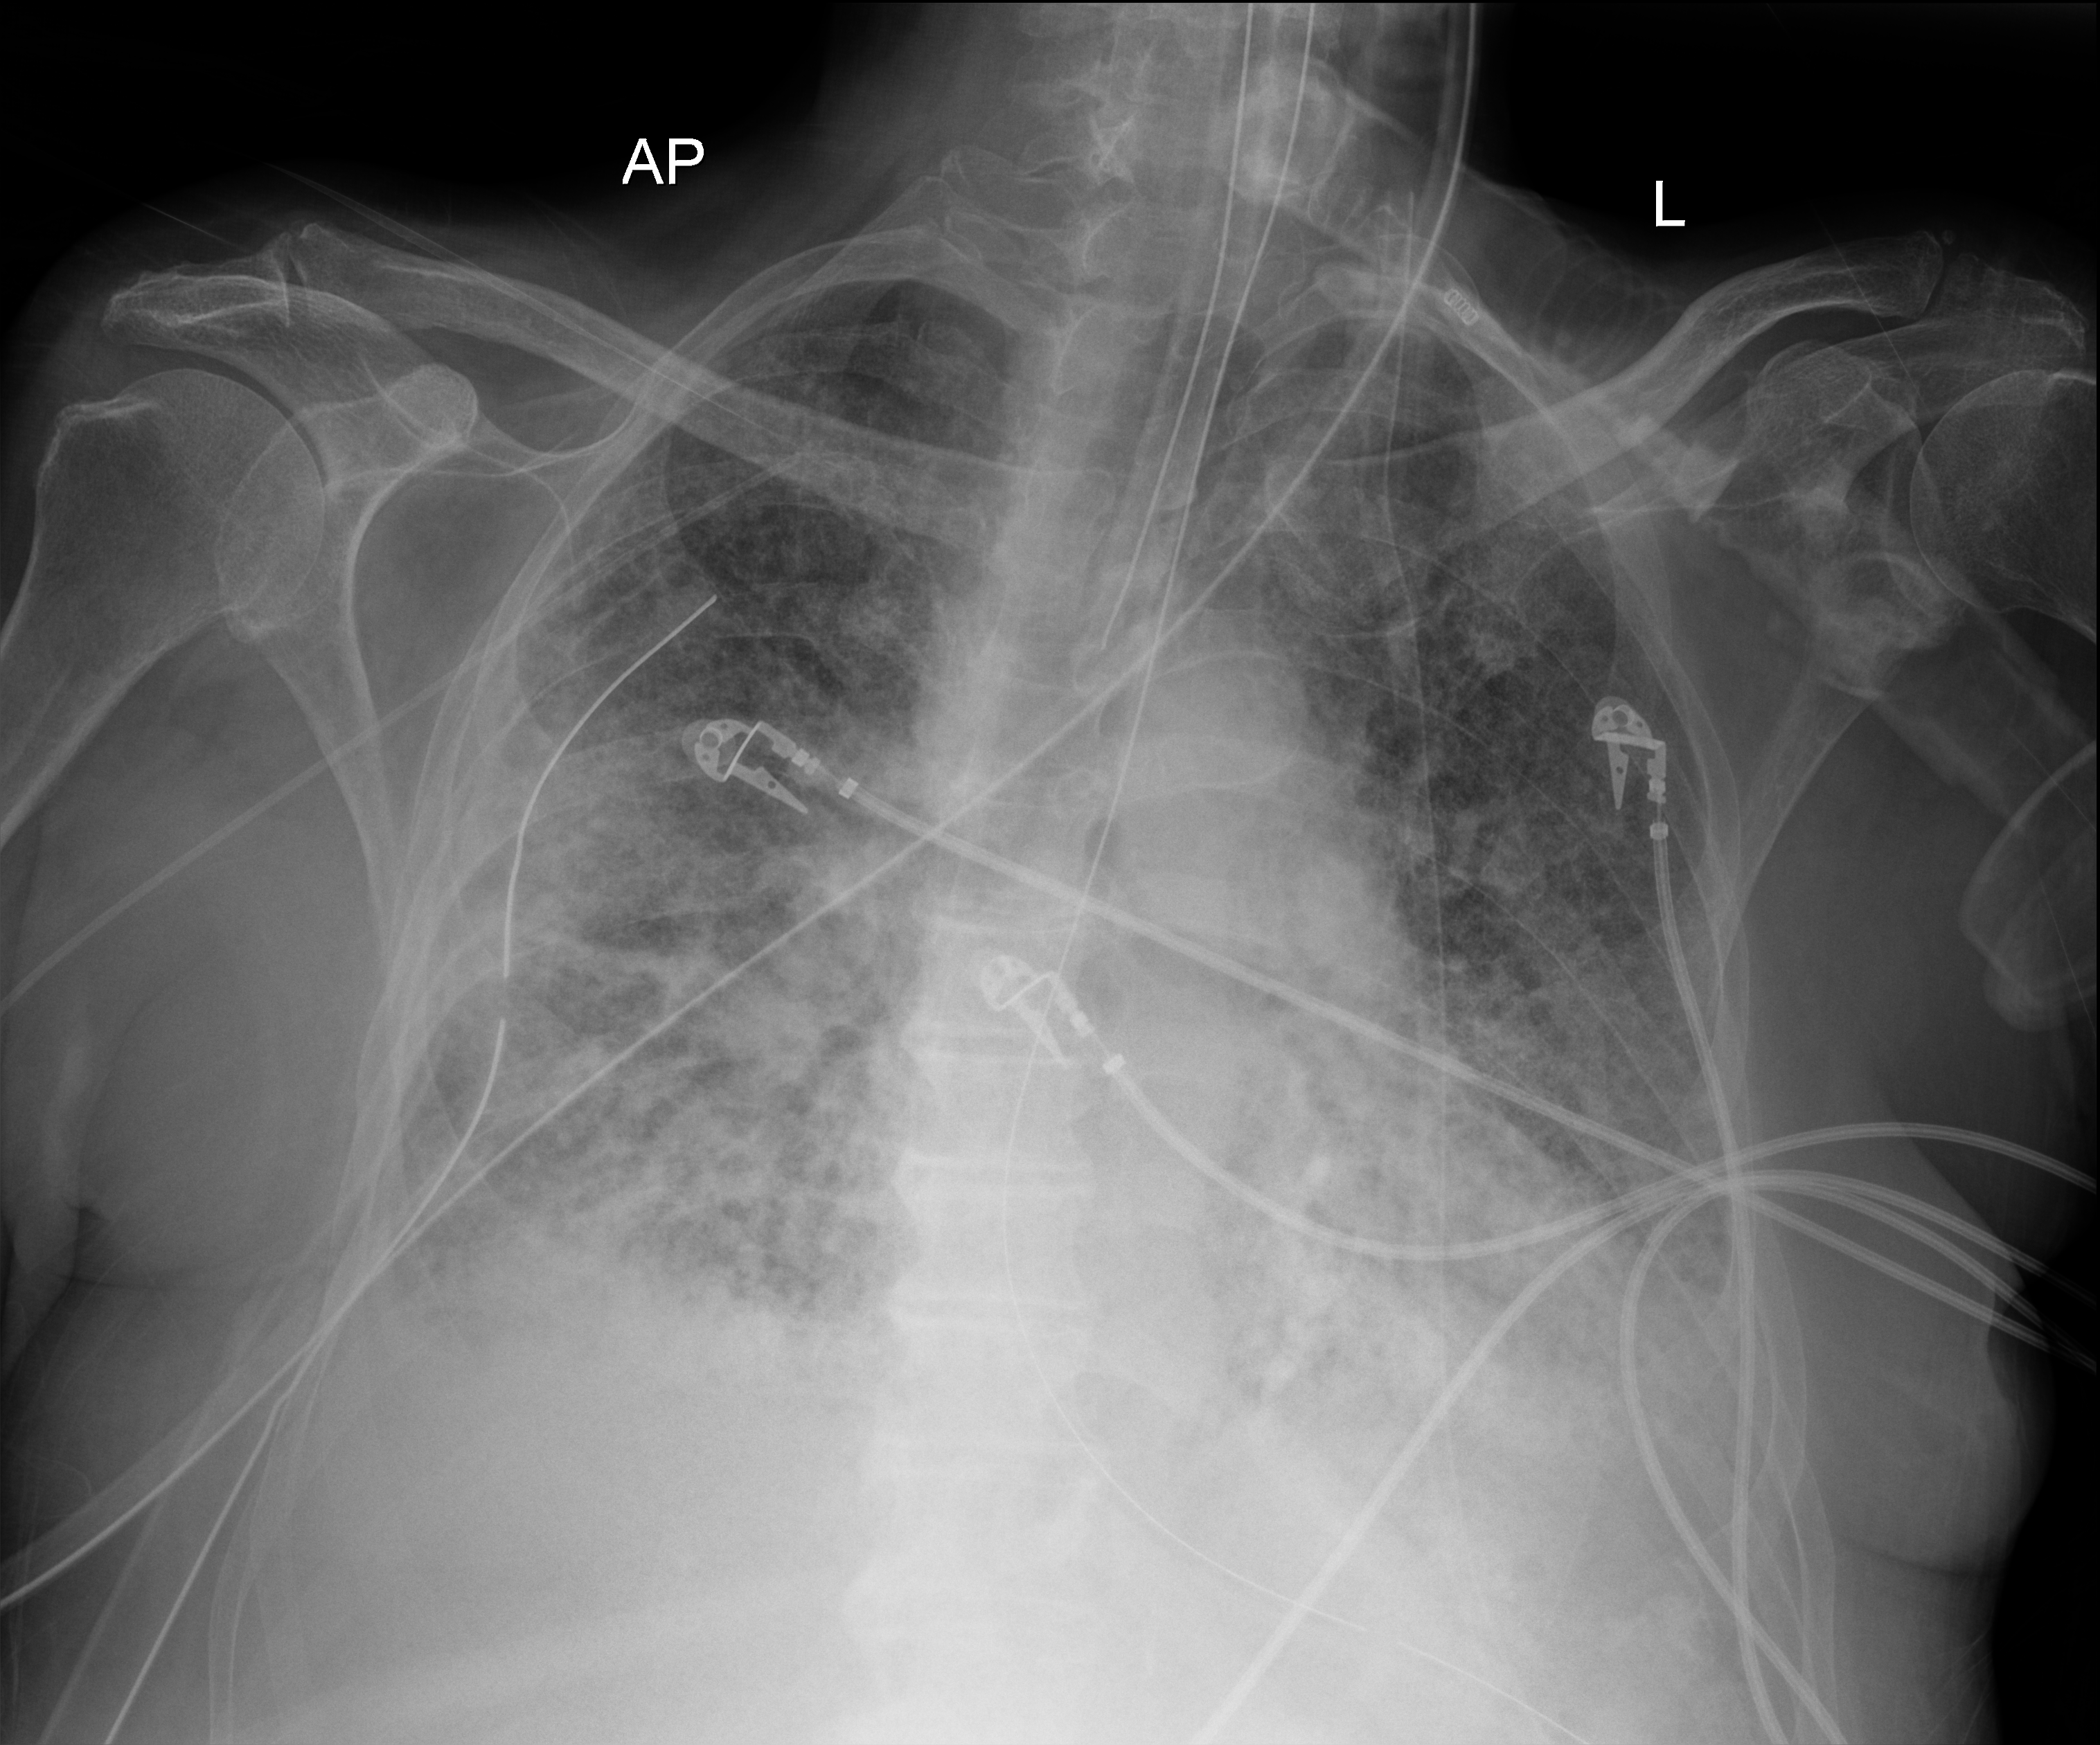
Portable chest radiograph, anteroposterior (AP) projection. Patient hospitalised with COVID-19; male, aged 75–90 years.
Admission-level facts for this patient (not findings on this image; timing relative to this image not recorded): admitted to intensive care during this hospital stay: yes; chronic kidney disease (admission record): no; smoking status (admission record): never.